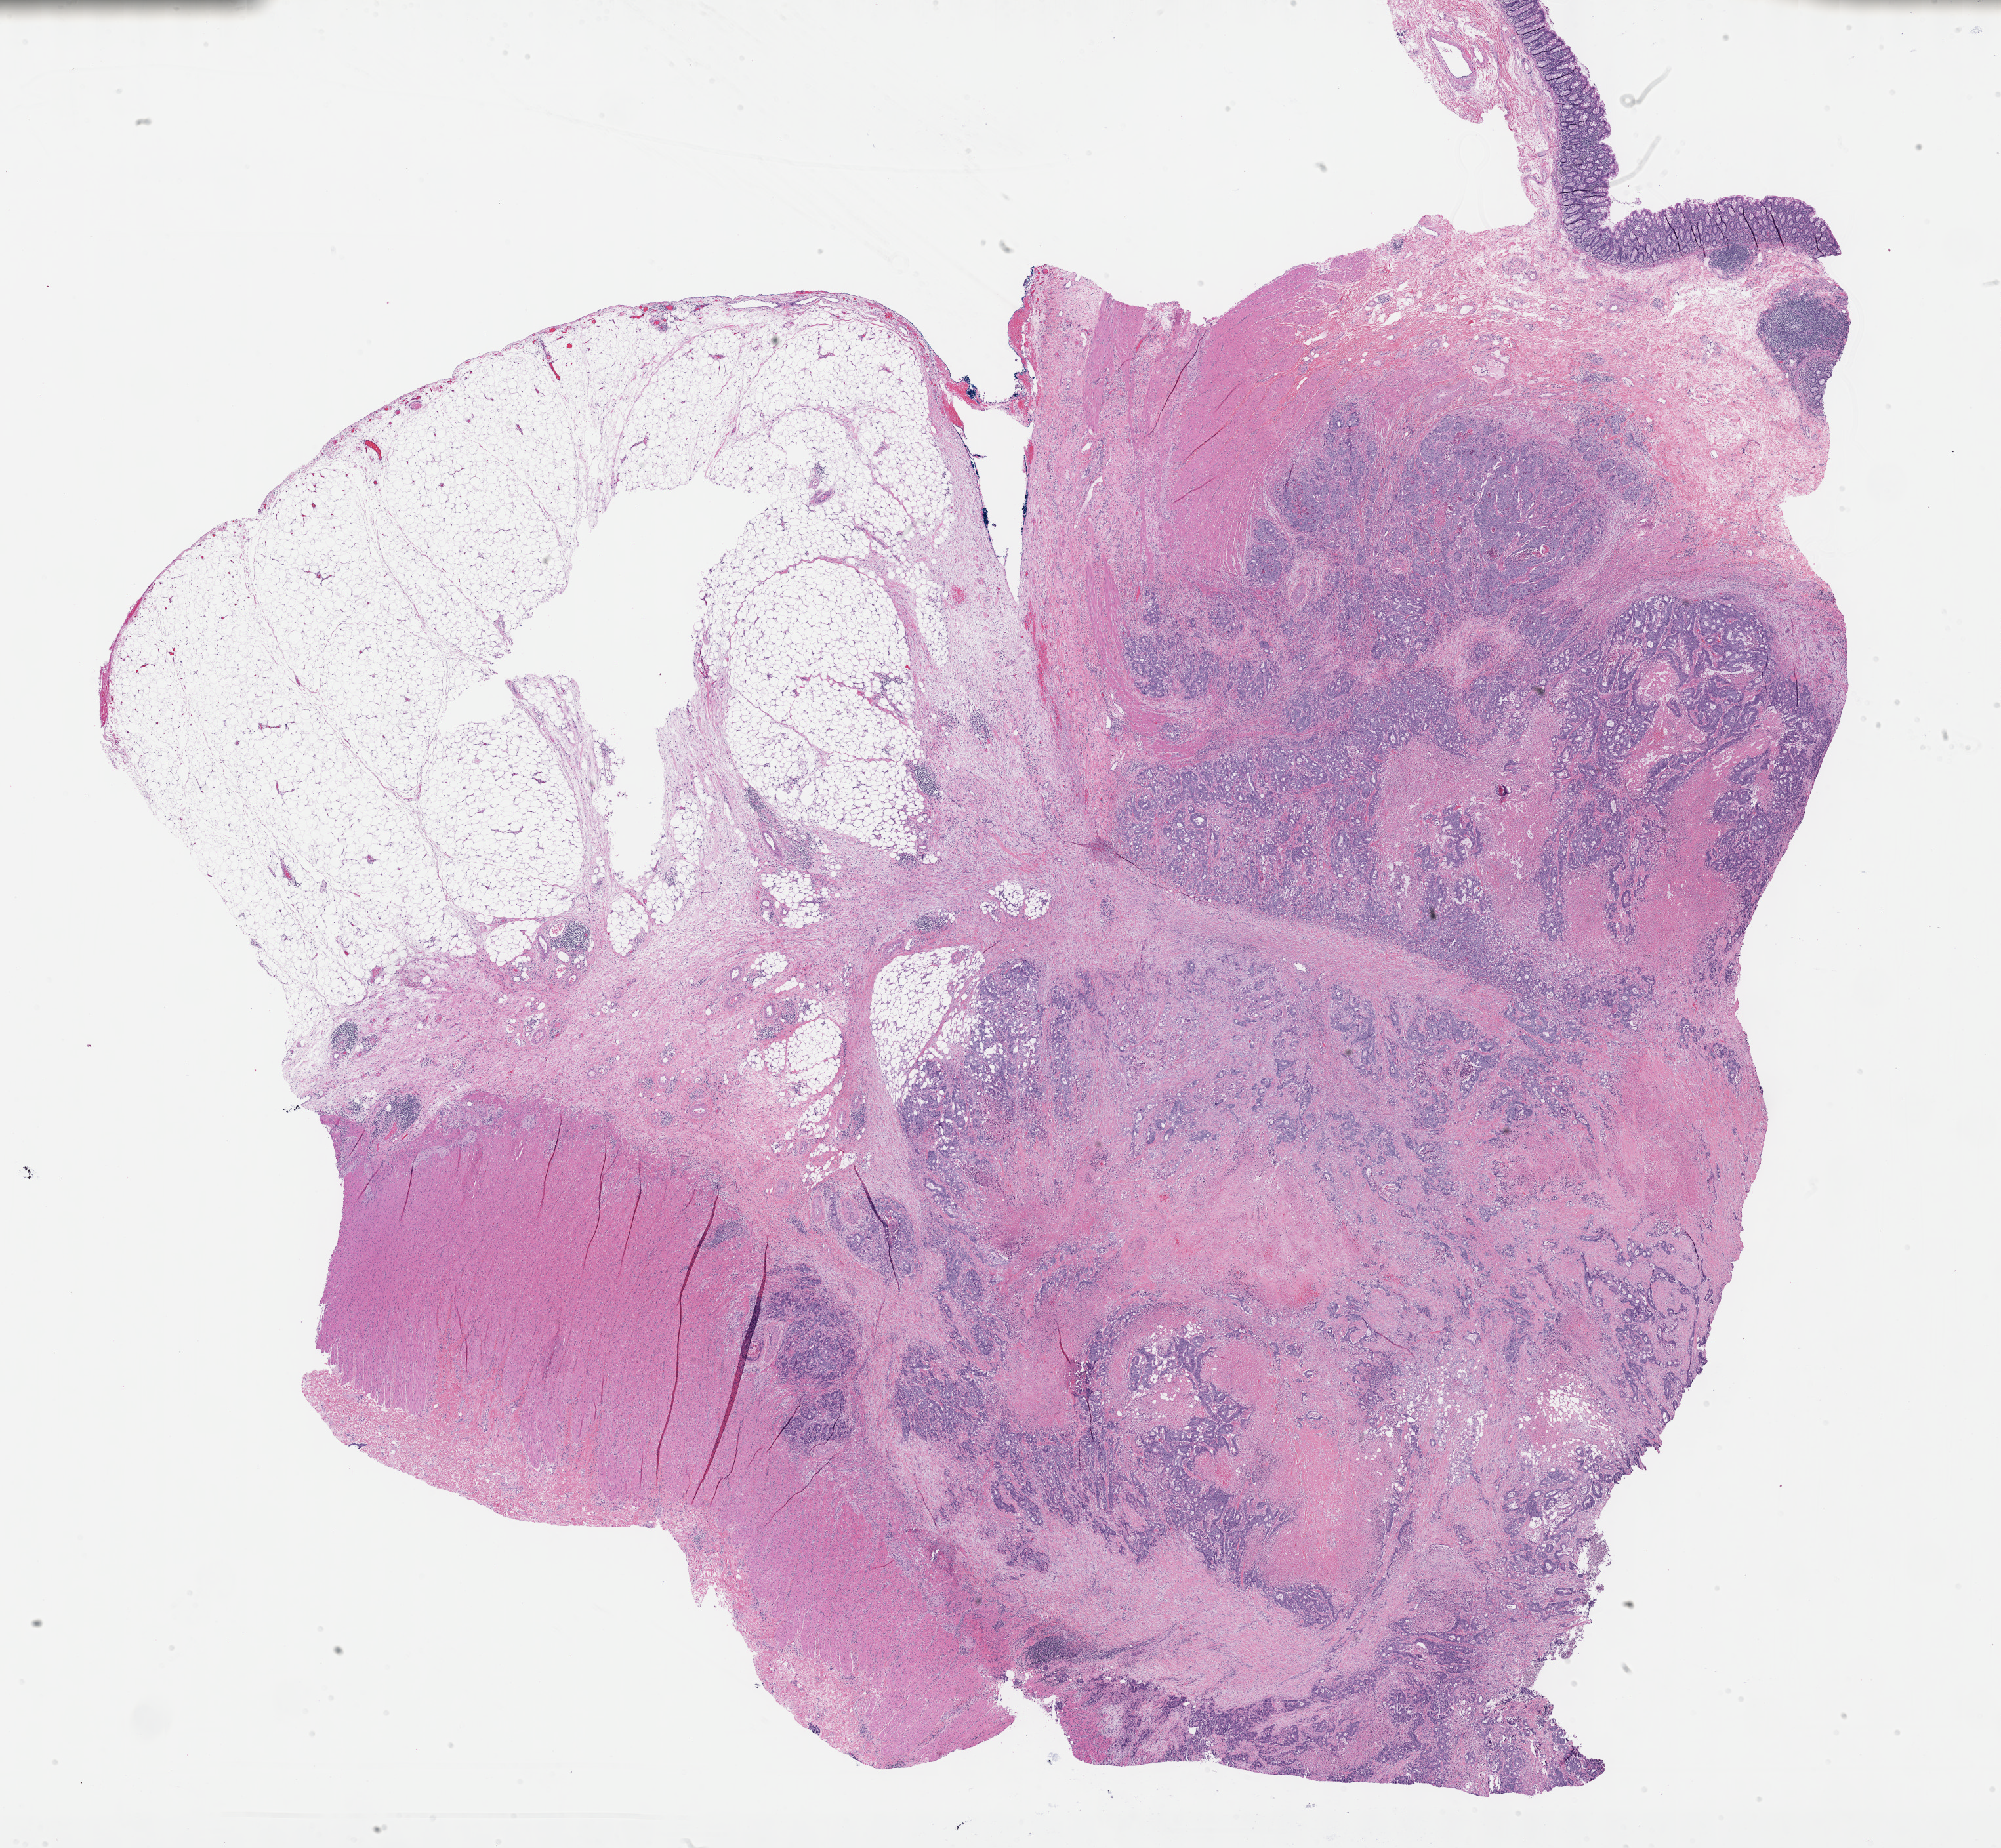
Digitized Hematoxylin and eosin (H&E) stained tissue section (whole slide), low-resolution overview of the scanned area, about 24.7 x 22.8 mm (from a 40x scan). Formalin-fixed paraffin-embedded (FFPE) diagnostic section. Primary tumour sample from the colon. Patient: male, age at initial diagnosis 79 years.
* pathologic diagnosis: Adenocarcinoma, NOS (ascending colon)
* lymph nodes positive (case pathology): 15 of 22 examined
* AJCC pathologic stage: IV (7th edition)